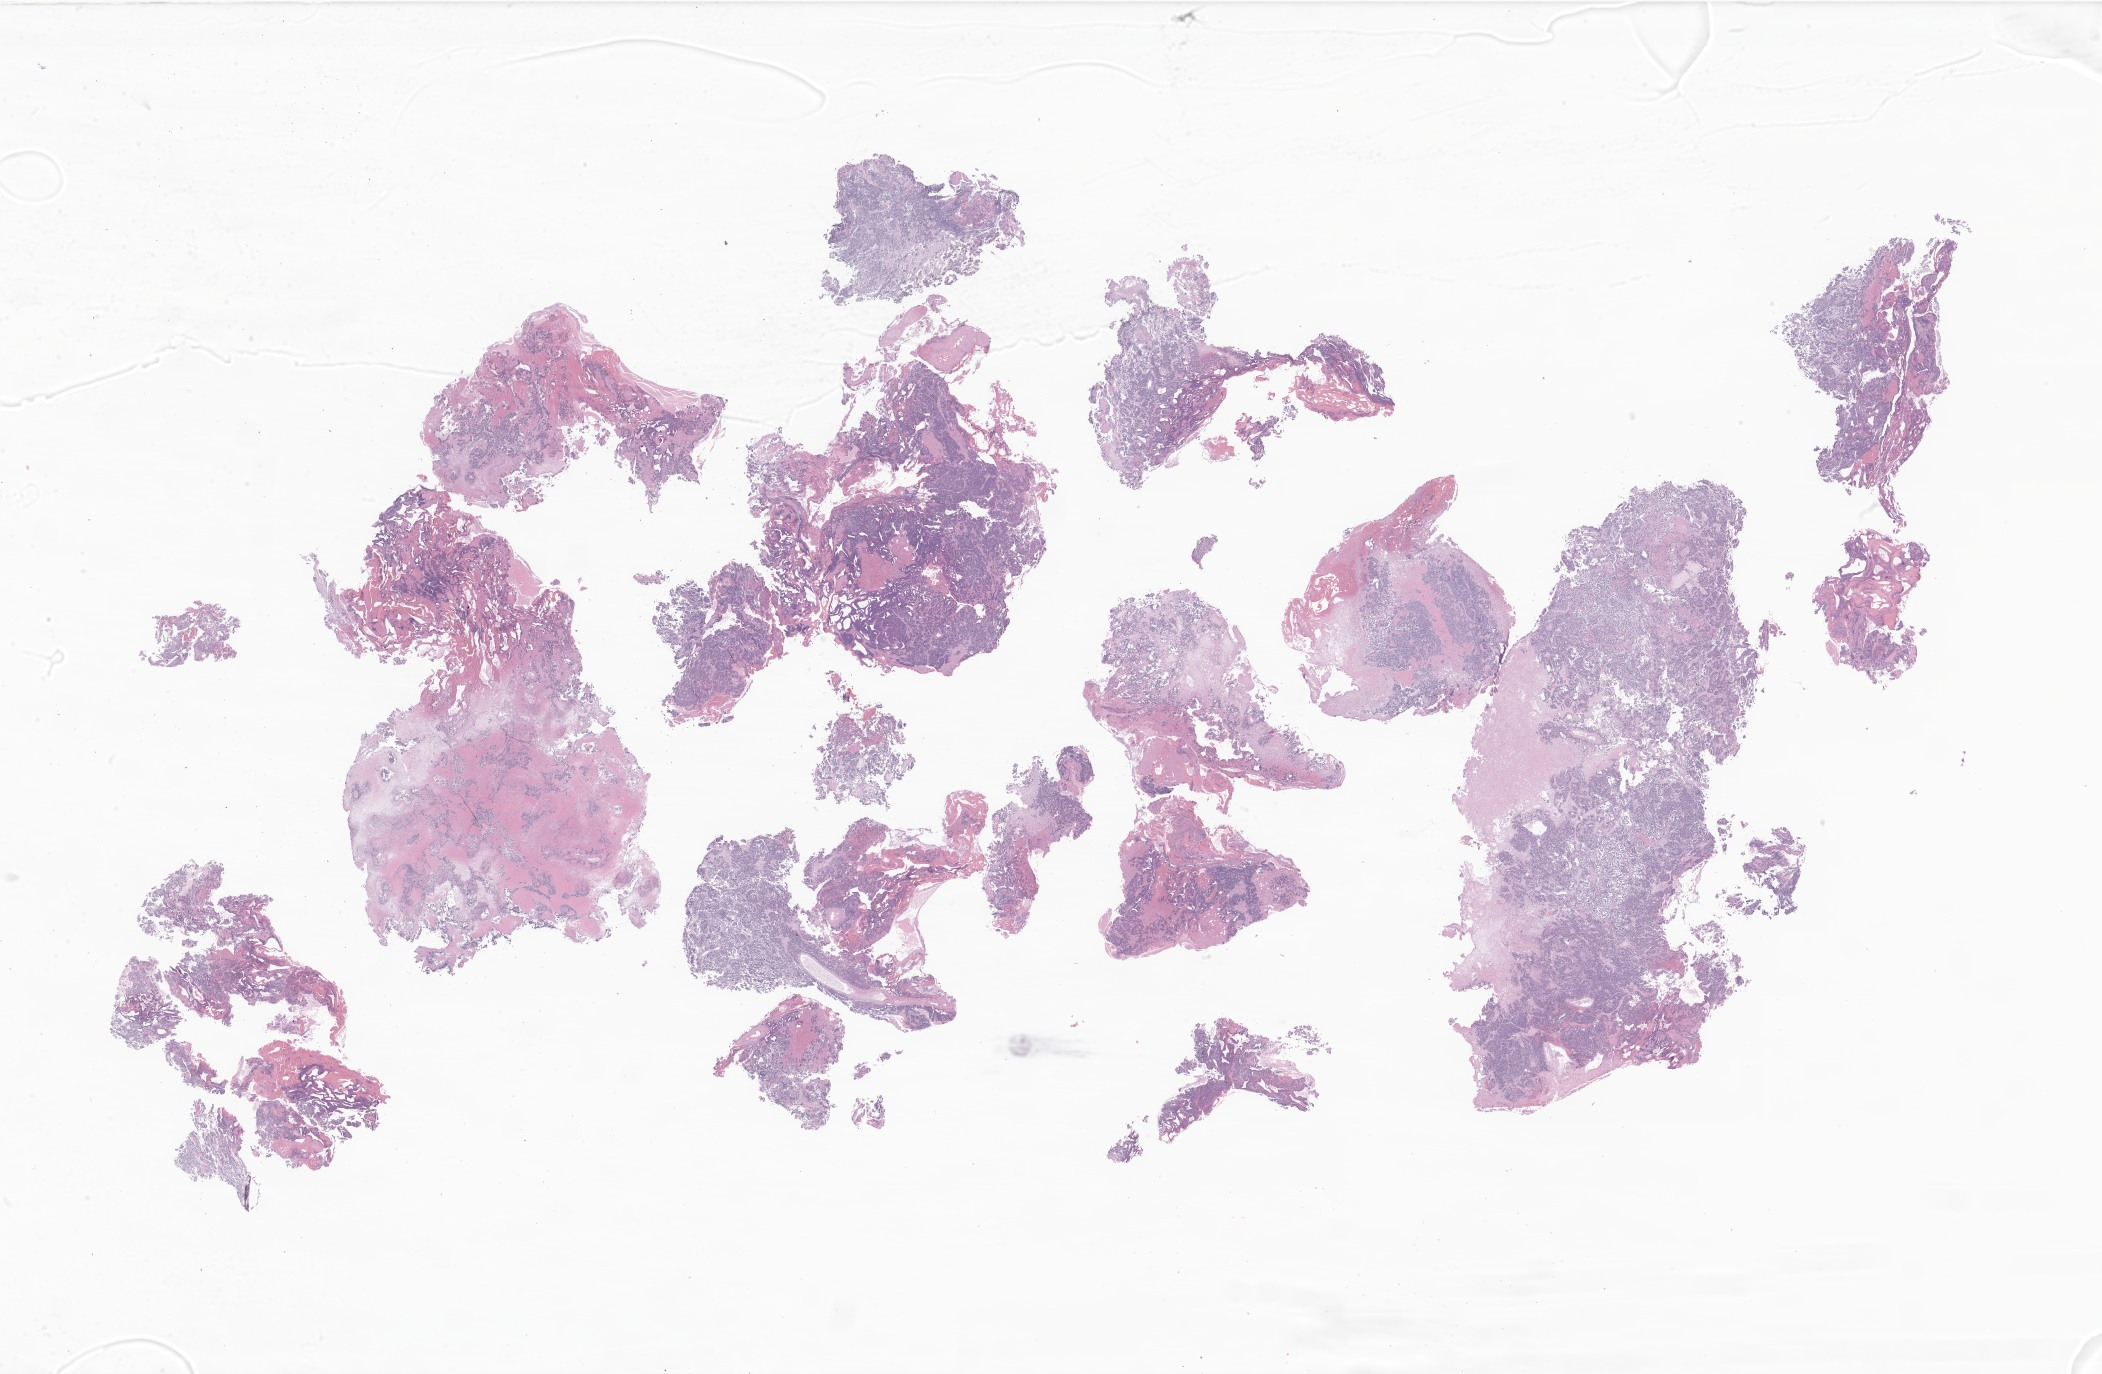
Digitized haematoxylin and eosin-stained section of tumor tissue from the brain, whole scanned area (about 35.5 x 23.2 mm) shown as a low-resolution overview, FFPE section. Patient female; age 261 months.
• diagnosis: Pineoblastoma